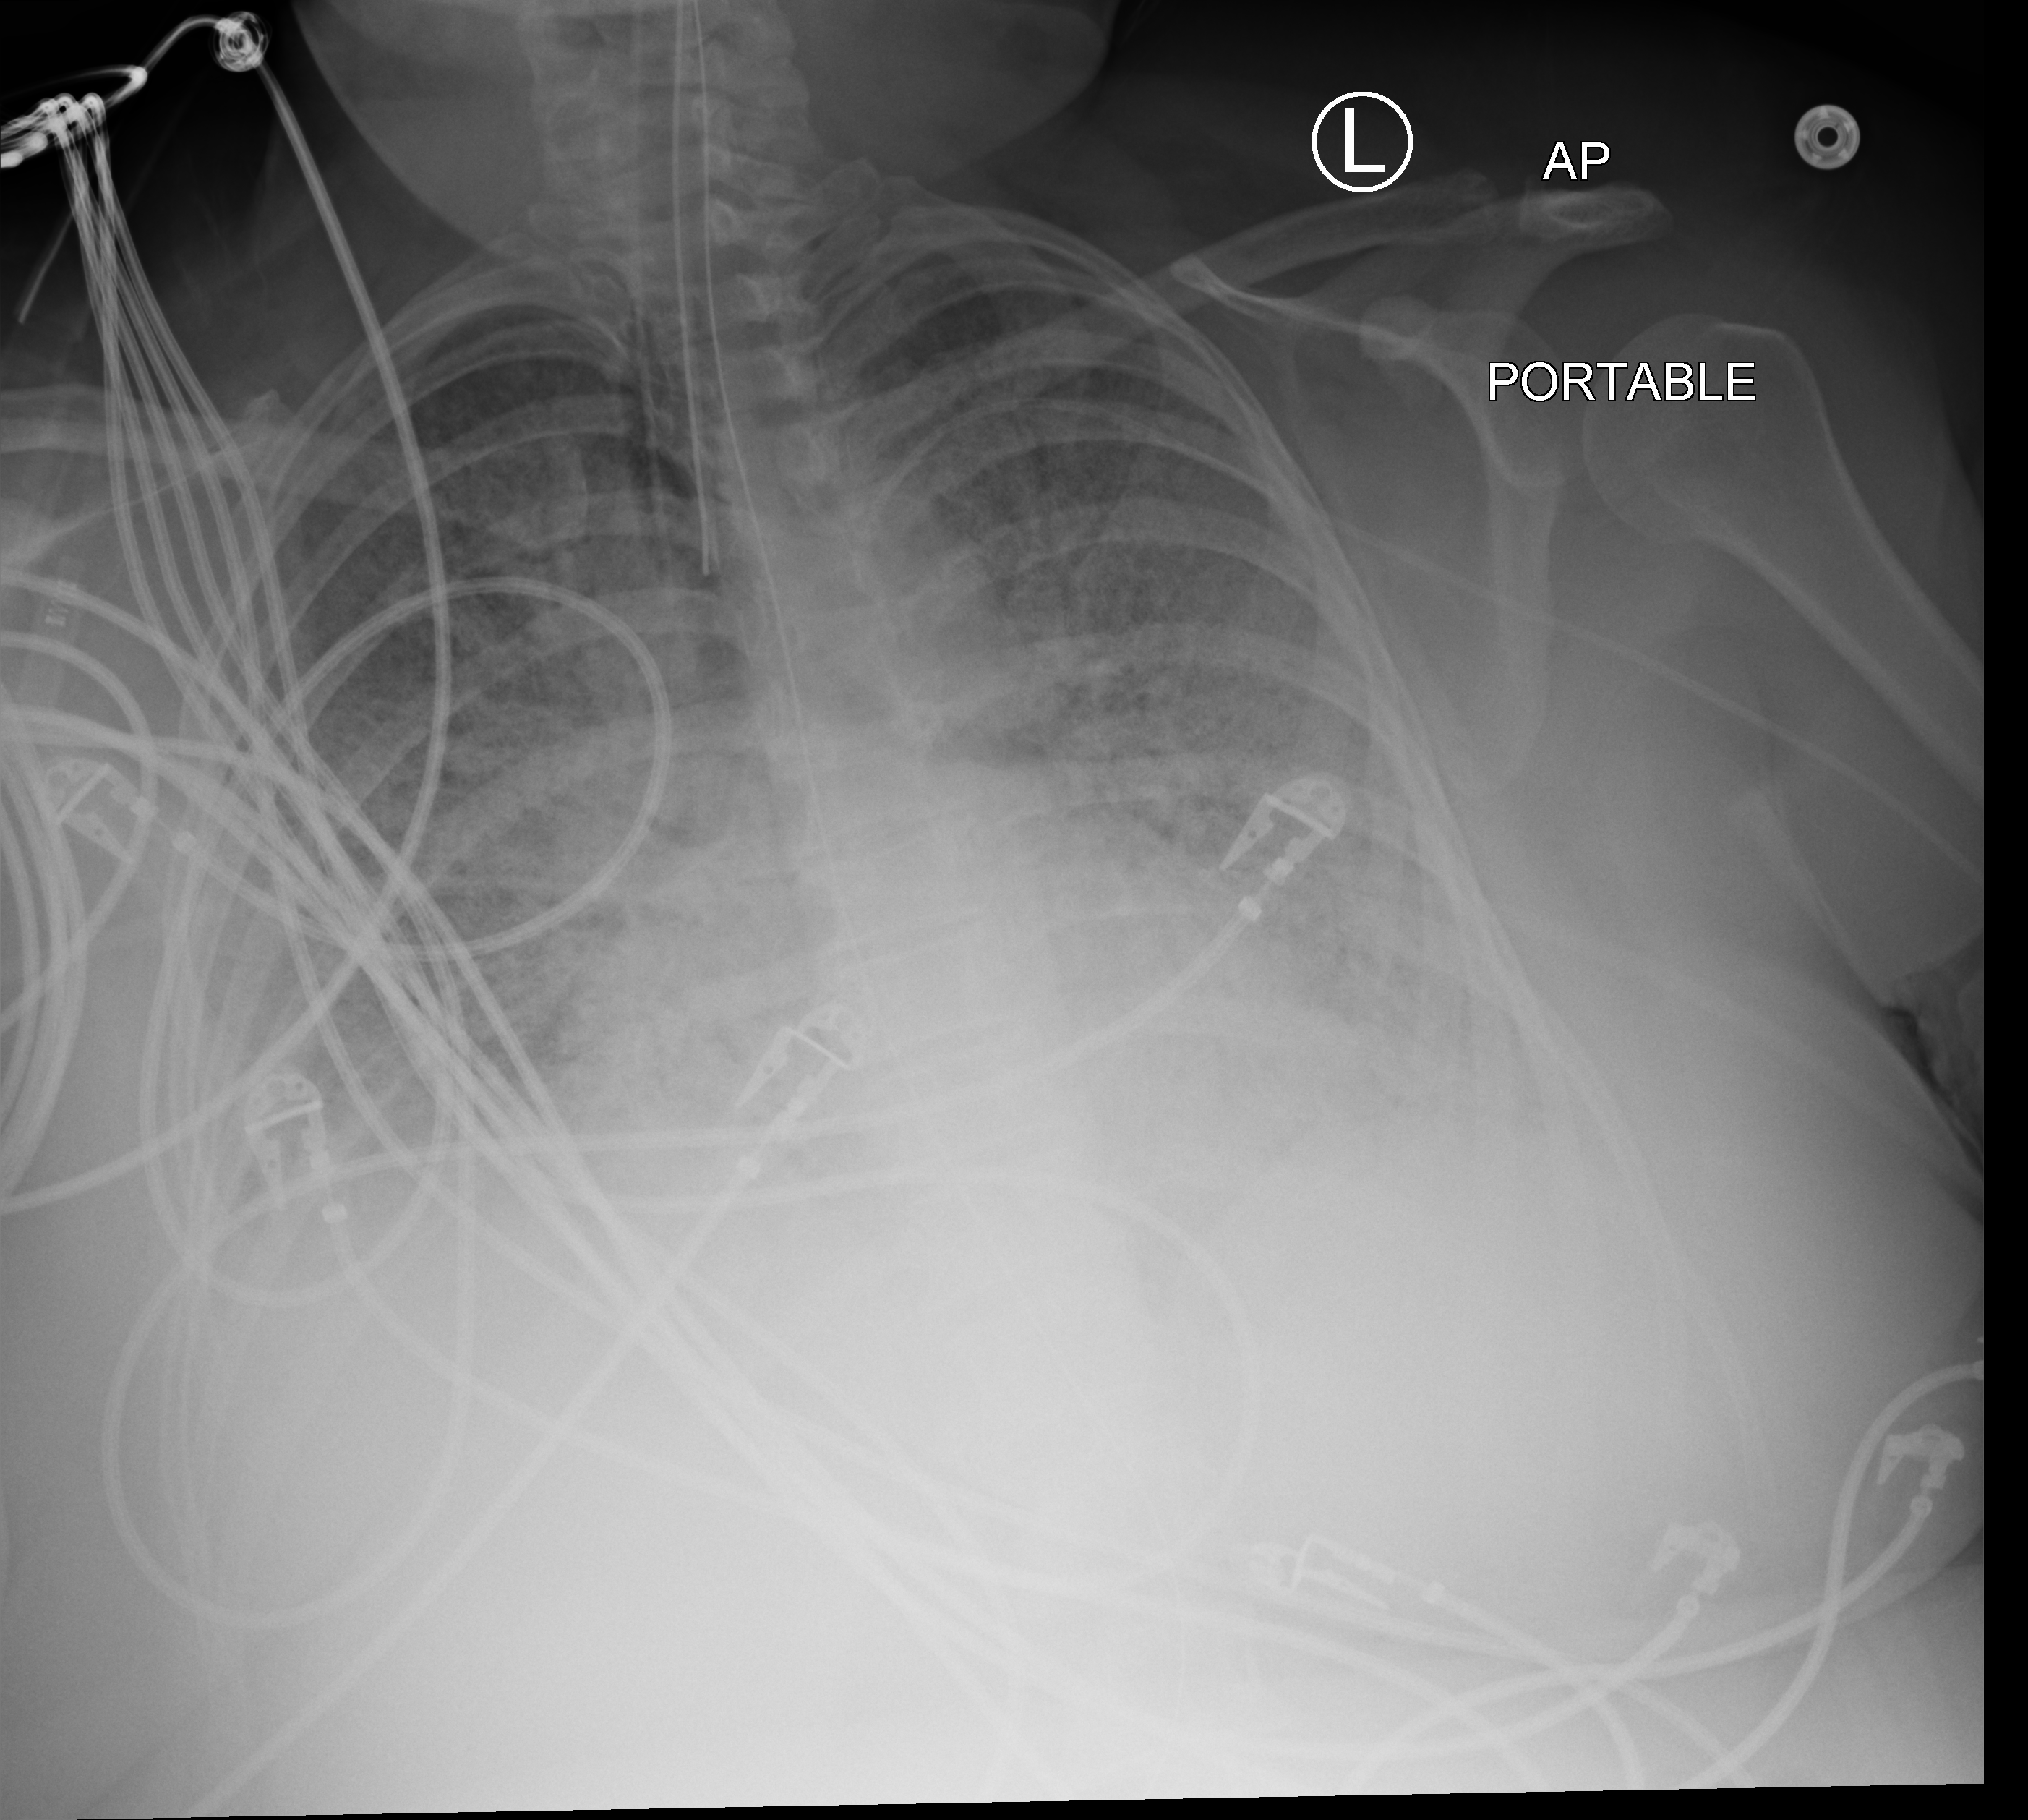
Chest X-ray (portable), anteroposterior (AP) projection. Female patient hospitalised with COVID-19, age 18–59 years.
Admission-level facts for this patient (not findings on this image; timing relative to this image not recorded): COPD (admission record): no; mechanically ventilated during this hospital stay: yes; admitted to intensive care during this hospital stay: yes.